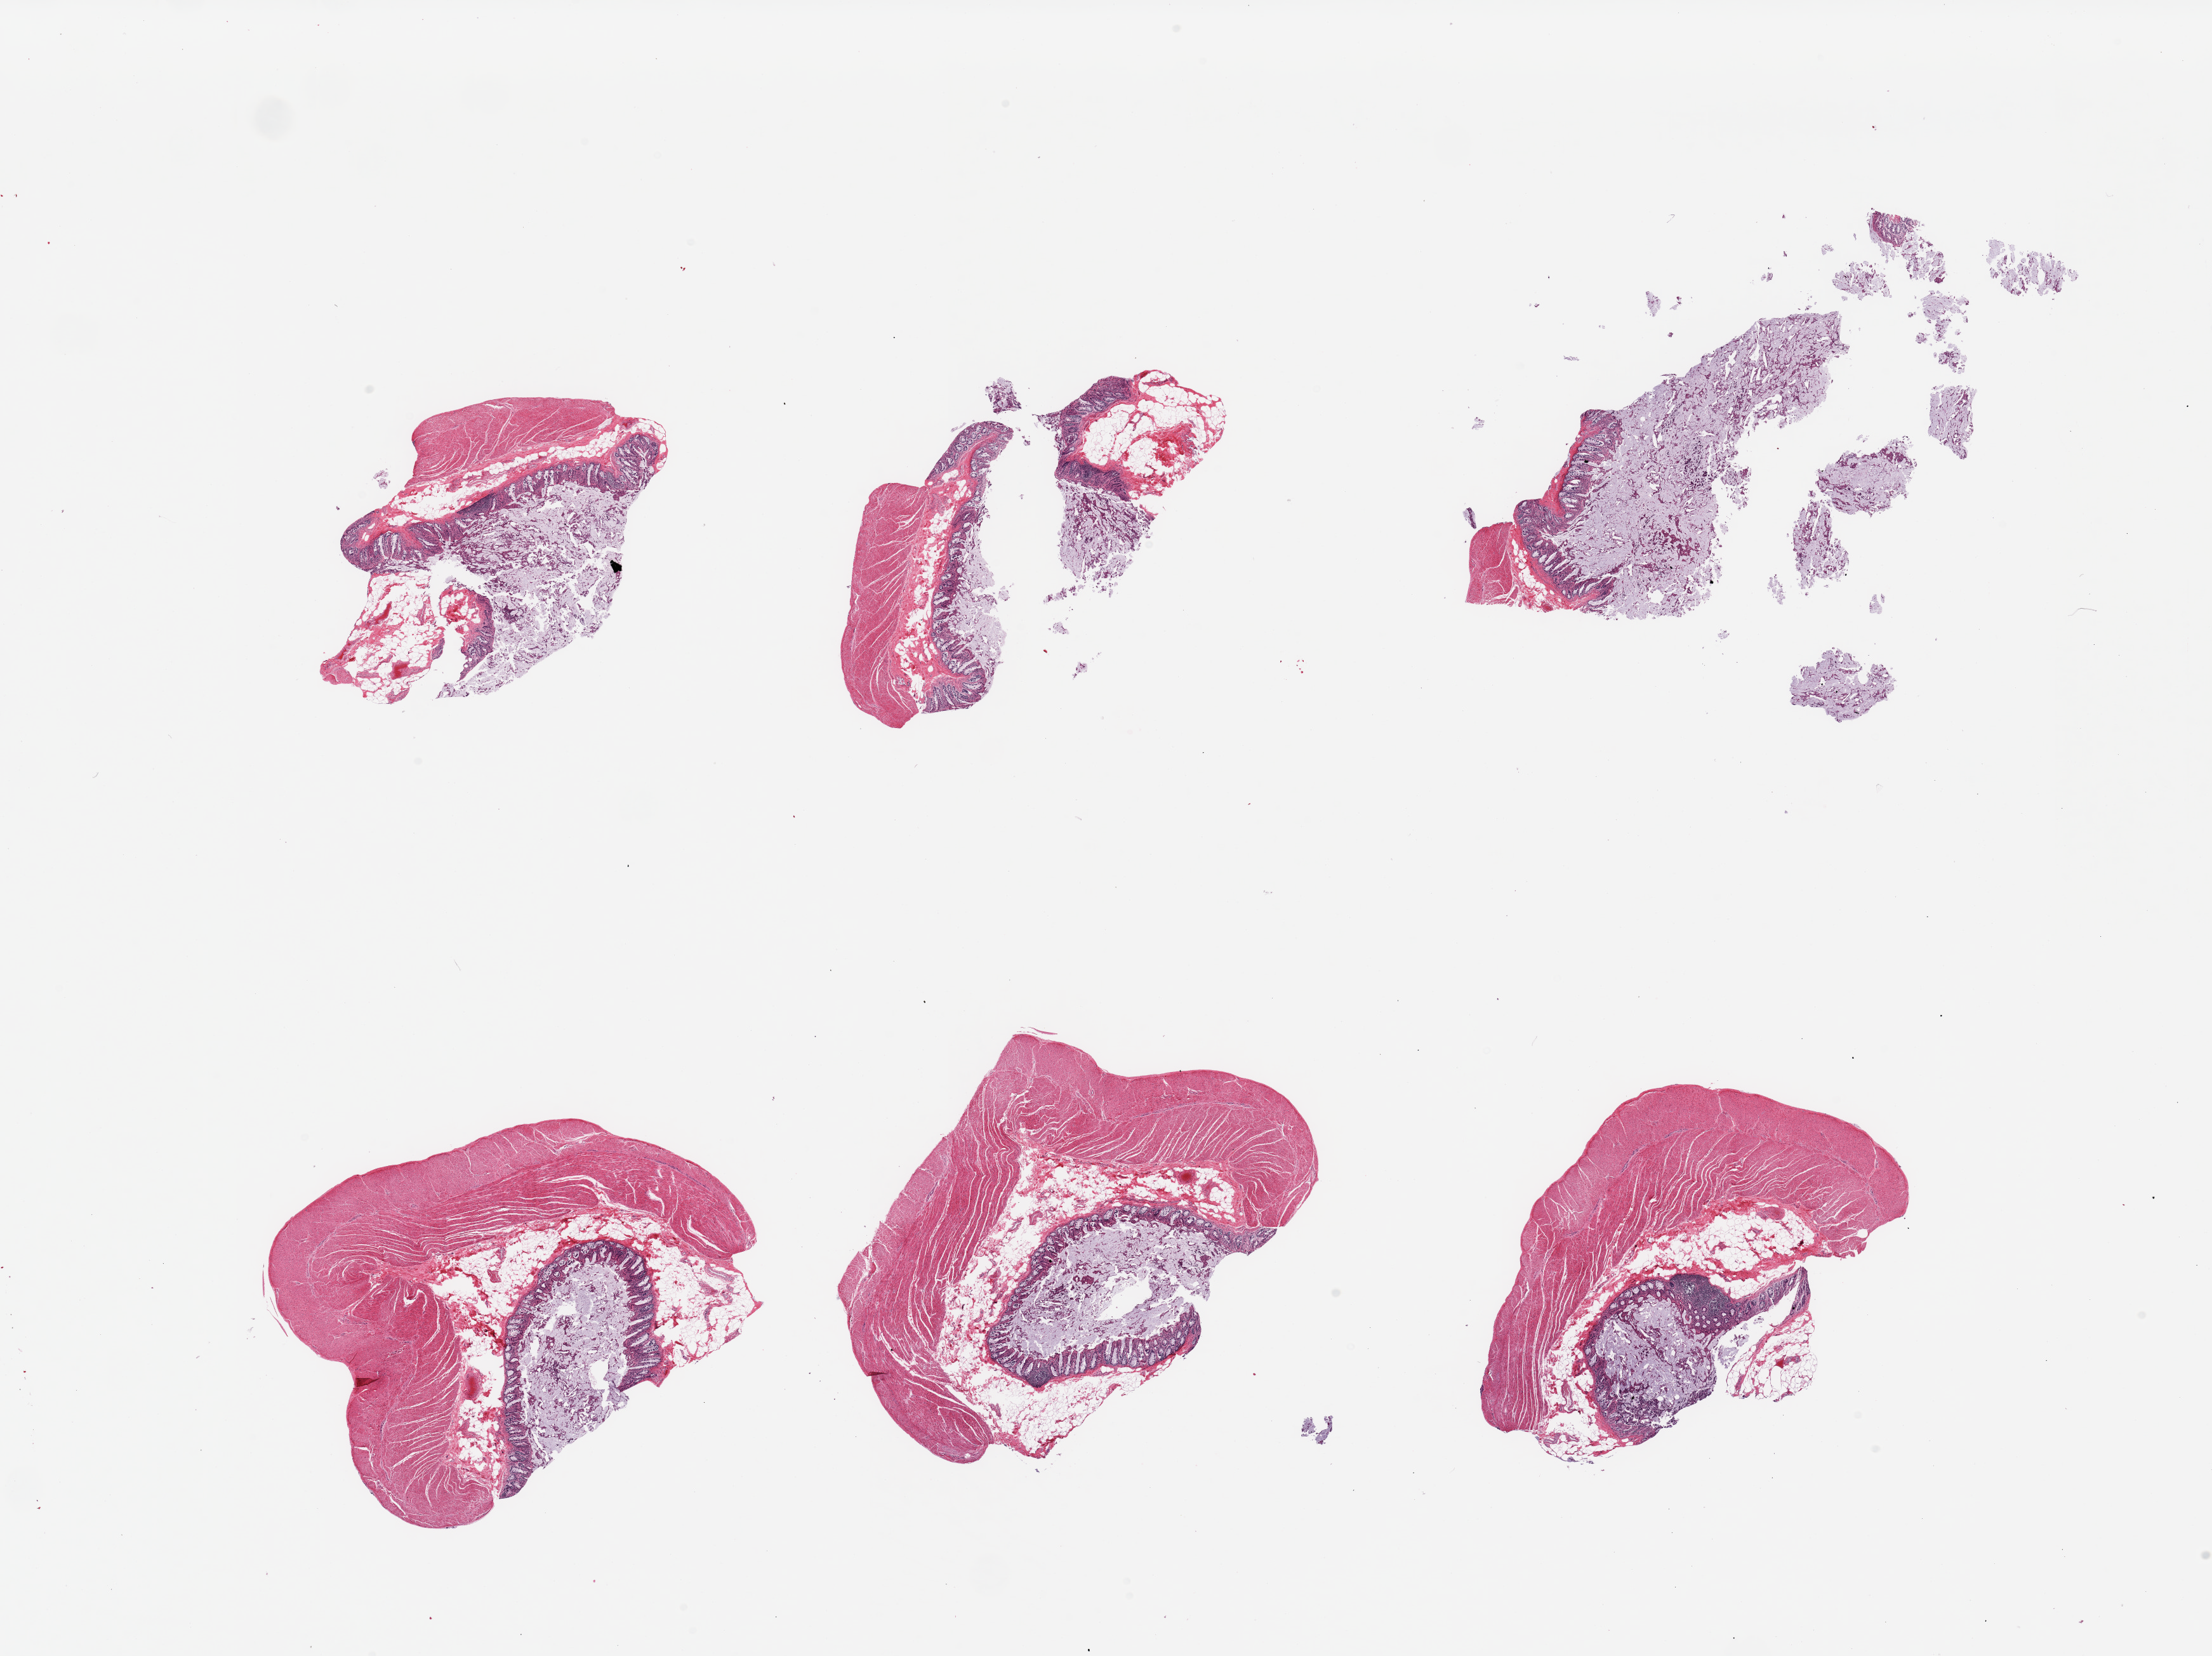
H&E whole-slide image — low-resolution overview of the scanned area, about 27.6 x 20.6 mm (slide scanned at 20x). PAXgene-fixed, paraffin-embedded tissue. Target tissue: ileum. Tissue donor sample. Donor: male.
Review note (as recorded): 6 pieces; muscularis propria present in all; minimal lymphoid tissue content.